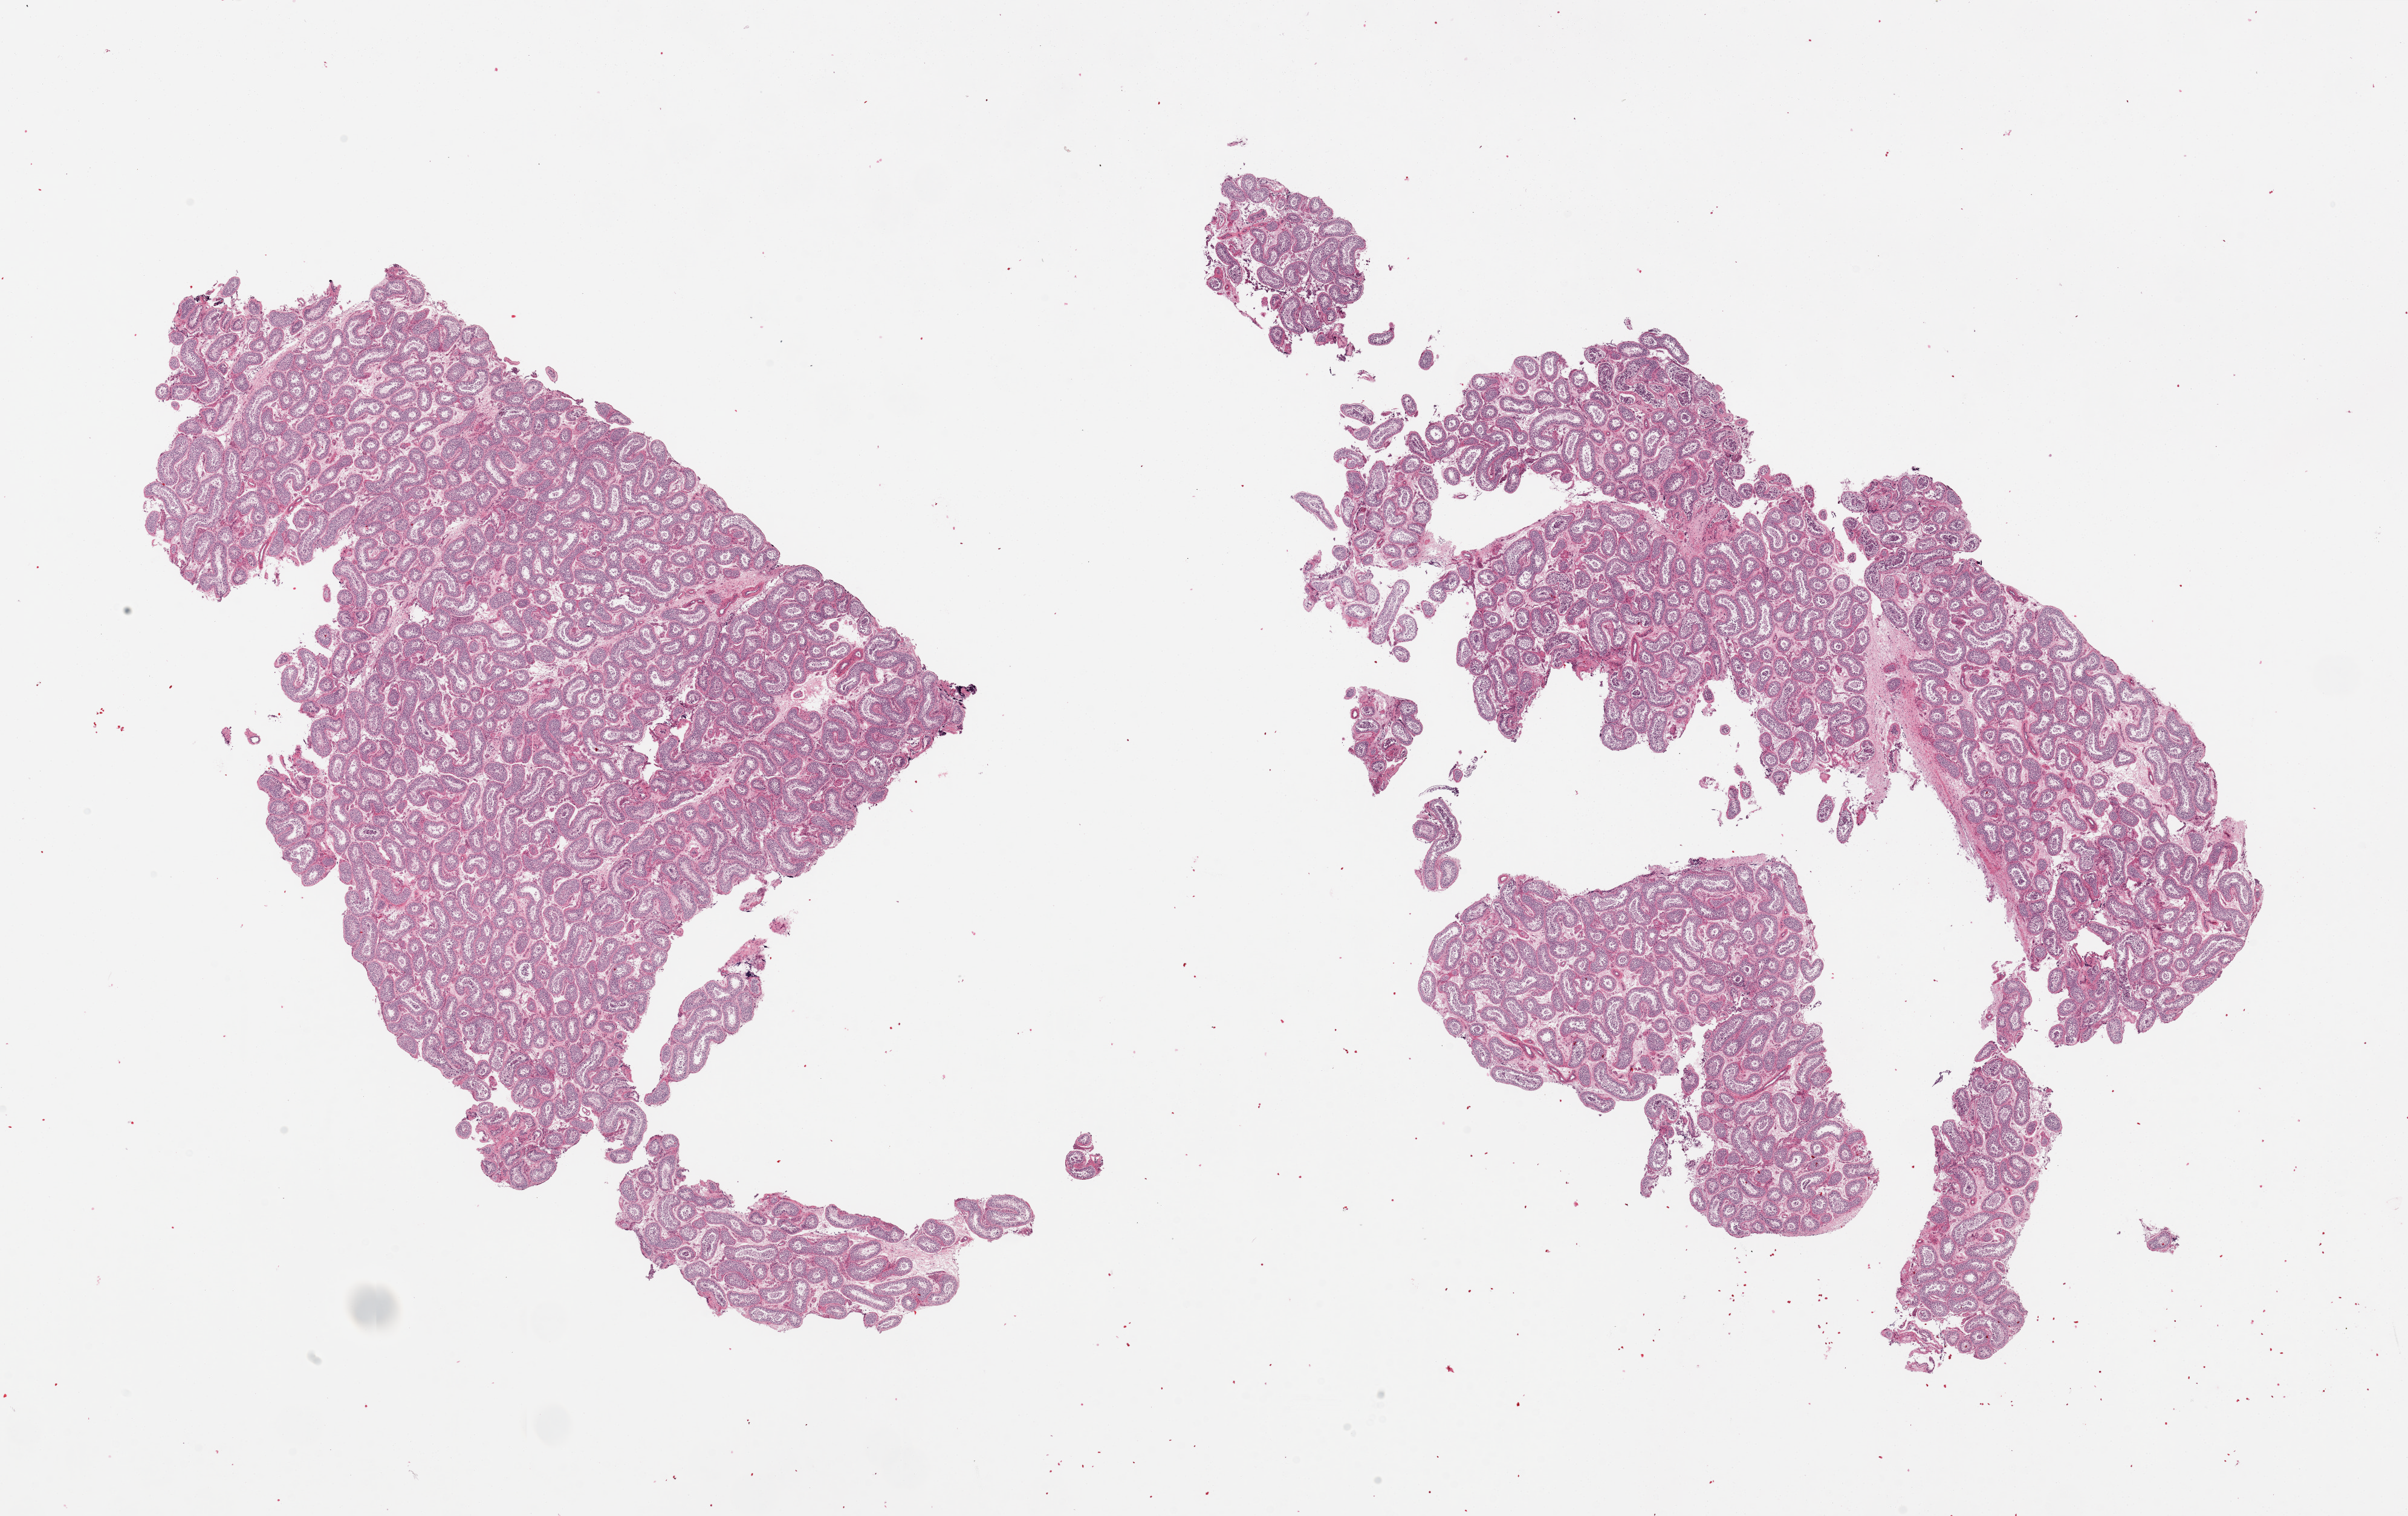
Whole-slide image, H&E stain, brightfield — a low-resolution overview of the entire scanned area, about 31.5 x 19.8 mm. PAXgene-fixed paraffin-embedded (PFPE) section. Section of testis (target tissue). Donor tissue sample. Donor: male.
Review note (as recorded): 2 pieces, well-preserved. Spermatogenesis is present.